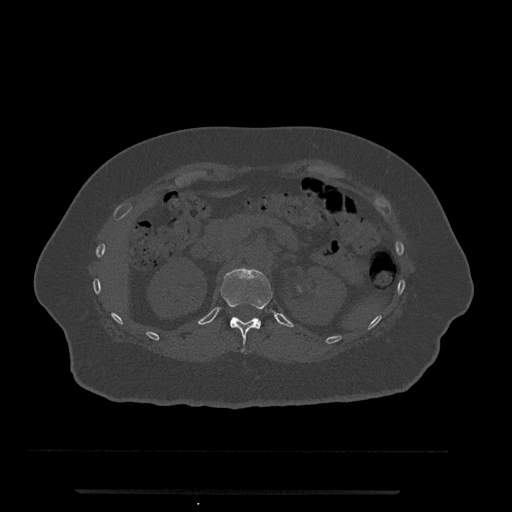
CT including the spine, one axial slice; slice 160 of 797 in the series (ordered by position); reconstruction kernel Br40s/3; 120 kVp; bone window (W 1800 / L 400 HU); 0.5 mm slice thickness; 512 × 512 image matrix, field of view 440 × 440 mm. Patient: female, 51 years. Case-level facts recorded for this patient, not image findings: primary cancer: neuro; vertebrae with lytic lesions (as recorded): T8.
Annotated regions visible in this slice (semi-automatic segmentation, software-assisted and operator-edited):
- T12 vertebra: bounding box (x1, y1, x2, y2) in pixels: (221, 267, 273, 351)